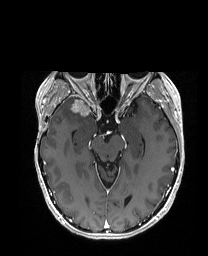
Brain MRI from a brain-tumour surgery series, one axial slice. Position 110 of 192 along the scan axis. T1-weighted post-contrast. 1 mm slice thickness. 208 × 256 image matrix, field of view 203 × 250 mm. From the clinical record (not read from this slice): histopathology: Metastatic Carcinoma from Breast primary; tumour location: Right Frontal.
Structures marked on this image (outlined manually by an expert reader):
- tumour: bounding box (x1, y1, x2, y2) in pixels: (67, 98, 88, 114)